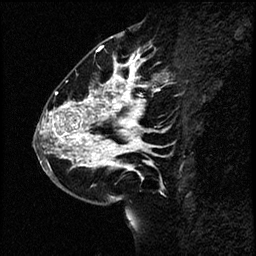
Breast MRI (dynamic contrast-enhanced), one sagittal slice; position 29 of 60 along the scan axis; dynamic contrast-enhanced study with each time point stored as its own series, time point 2 of 4 at this slice position (early post-contrast, ordered by acquisition time); 1.5 T; TE 4.2 ms, TR 17.6 ms; 256 × 256 image matrix, field of view 200 × 200 mm. Female patient, age 43 years. Case-level facts recorded for this patient, not image findings: setting: breast cancer imaged before/during neoadjuvant chemotherapy.
Annotated regions visible in this slice (semi-automatic segmentation, software-assisted and operator-edited):
- analysis volume of interest (the breast-tissue region the enhancement analysis was run in; not a lesion): bounding box [x1, y1, x2, y2] px = [35, 56, 169, 191]
- tumour enhancement mask (voxels above the 100 % enhancement threshold inside the analysis volume of interest): [40, 56, 157, 170]